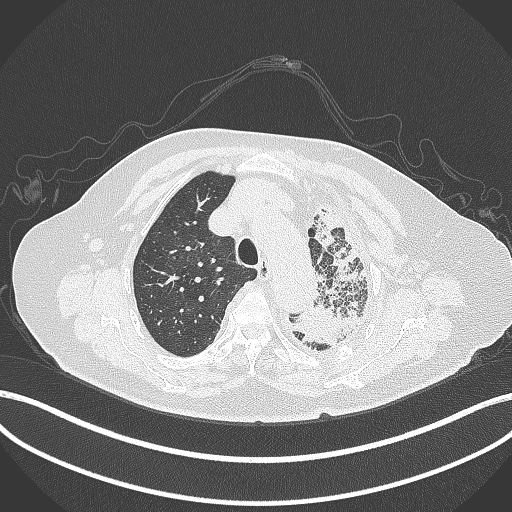
Chest CT, one axial slice. Position 304 of 399 along the scan axis. Reconstruction kernel B70f. 120 kVp. Lung window (W 1500 / L -600 HU). 1 mm slice thickness. 512 × 512 image matrix. Female patient, age 75 years. From the clinical record (not read from this slice): clinical TNM (as recorded): T3 N3 M1.
Outlined on this slice (rectangle marked by the reading radiologist):
- lung tumour (recorded histology: adenocarcinoma): bounding box <293,294,369,348> (left, top, right, bottom; pixels)